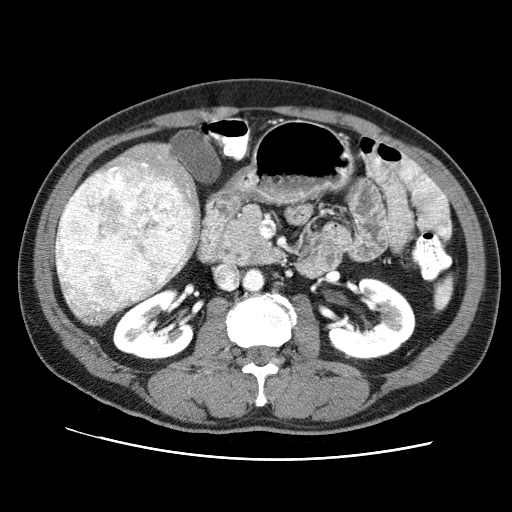
Contrast-enhanced abdominal CT (liver protocol), one axial slice; position 29 of 71 along the scan axis; reconstruction kernel STANDARD; soft-tissue window (W 400 / L 40 HU); 512 × 512 image matrix, field of view 360 × 360 mm. Case-level facts recorded for this patient, not image findings: diagnosis: hepatocellular carcinoma (patient treated with transarterial chemoembolisation; whether this scan precedes or follows treatment is not stated here); TNM stage (as recorded): Stage-II; Child-Pugh class: A; tumour differentiation: well differentiated; tumour nodularity: multinodular.
Structures marked on this image (semi-automatically segmented with operator editing):
- liver parenchyma outside the tumour (the mass and vessels are separate outlines, so this box may not span the whole liver): bounding box [x1, y1, x2, y2] px = [58, 142, 200, 302]
- mass: [55, 163, 194, 326]
- liver vessels: [112, 157, 189, 192]